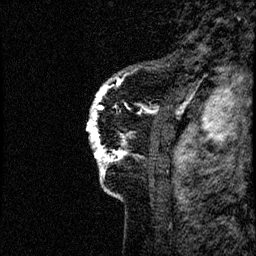
Breast MRI (dynamic contrast-enhanced), one sagittal slice. Position 9 of 60 along the scan axis. Dynamic contrast-enhanced study with each time point stored as its own series, time point 2 of 4 at this slice position (early post-contrast, ordered by acquisition time). 1.5 T. TE 4.2 ms, TR 17.6 ms. 2 mm slice thickness. 256 × 256 image matrix, field of view 200 × 200 mm. Female patient, age 40 years. Case-level facts recorded for this patient, not image findings: setting: breast cancer imaged before/during neoadjuvant chemotherapy; receptor status: HER2-positive.
Annotated regions visible in this slice (semi-automatically segmented with operator editing):
- analysis volume of interest (the breast-tissue region the enhancement analysis was run in; not a lesion): box from (x=84, y=56) to (x=185, y=206) px
- tumour enhancement mask (voxels above the 100 % enhancement threshold inside the analysis volume of interest): (x=87, y=87)–(x=158, y=172)